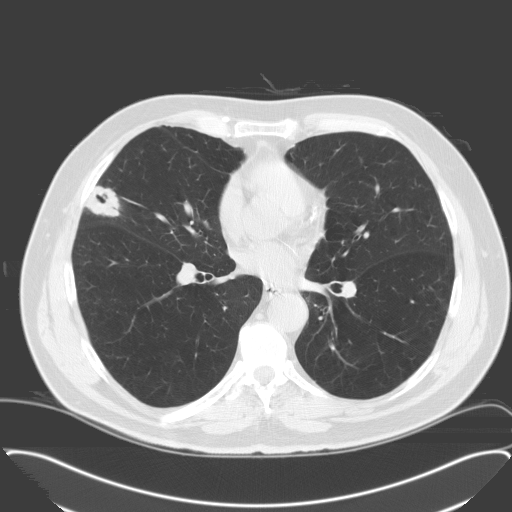
Axial slice from a low-dose chest CT screening exam, third annual screen, lung window (W 1500 / L -600 HU), 3.2 mm slice thickness, standard (soft-tissue) reconstruction kernel (C), 512 × 512 image matrix, field of view 400 × 400 mm. Male, age 65 years at enrolment. Former smoker at enrolment.
Lesion marked by an expert reader, bounding box <69,176,130,231> (left, top, right, bottom; pixels). Reader record for this screening exam (exam-level; its link to the box is not recorded): non-calcified nodule or mass ≥4 mm, right middle lobe, 28 × 23 mm, spiculated (stellate) margins, soft tissue attenuation, pre-existing on the prior screen: no. Participant outcome: lung cancer diagnosed 25 days after this screen — adenocarcinoma, NOS, right middle lobe, moderately differentiated (G2), stage IA (AJCC 6th edition), 25 mm at pathology.